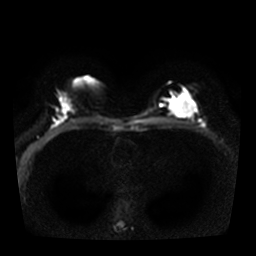
Breast MRI, one axial slice. Position 17 of 36 along the scan axis. Diffusion-weighted series; image 2 of 4 stored at this slice position (different b-values; order by instance number). 3 T. 5 mm slice thickness. 256 × 256 image matrix, field of view 320 × 320 mm. Female patient.
Outlined on this slice (outlined manually by an expert reader):
- tumour on diffusion-weighted imaging: bounding box <169,91,195,116> (left, top, right, bottom; pixels)